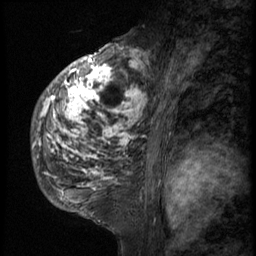
Breast MRI (dynamic contrast-enhanced), one sagittal slice. Slice 35 of 58 in the series (ordered by position). 3 images stored at this slice position (order not interpretable as contrast timing). 1.5 T. TE 4.2 ms, TR 9 ms. 2.5 mm slice thickness. 256 × 256 image matrix, field of view 180 × 180 mm. Female patient, age 50 years. From the clinical record (not read from this slice): setting: breast cancer imaged before/during neoadjuvant chemotherapy; receptor status: triple-negative.
Annotated regions visible in this slice (semi-automatic segmentation, software-assisted and operator-edited):
- analysis volume of interest (the breast-tissue region the enhancement analysis was run in; not a lesion): bounding box [x1, y1, x2, y2] px = [32, 48, 142, 214]
- tumour enhancement mask (voxels above the 140 % enhancement threshold inside the analysis volume of interest): [34, 48, 142, 190]